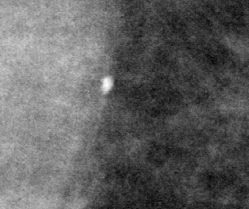
Crop from a digitized film mammogram around one marked abnormality; left breast; MLO view.
Calcifications, morphology punctate; BI-RADS assessment category 2; benign; no additional work-up was recommended (benign without callback).